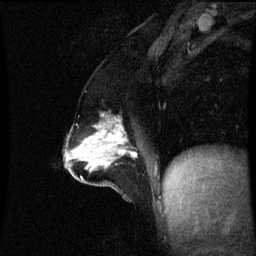
Breast MRI (dynamic contrast-enhanced), one sagittal slice. Slice 30 of 60 in the series (ordered by position). Dynamic contrast-enhanced series, image 2 of 3 at this slice position (ordered by acquisition). 1.5 T. TE 4.2 ms, TR 8.9 ms. 2.1 mm slice thickness. 256 × 256 image matrix. Patient: female, 47 years. Case-level facts recorded for this patient, not image findings: setting: breast cancer imaged before/during neoadjuvant chemotherapy; receptor status: HR-positive, HER2-negative.
Annotated regions visible in this slice (semi-automatic segmentation, software-assisted and operator-edited):
- analysis volume of interest (the breast-tissue region the enhancement analysis was run in; not a lesion): bounding box <71,120,138,163> (left, top, right, bottom; pixels)
- tumour enhancement mask (voxels above the 70 % enhancement threshold inside the analysis volume of interest): <88,124,138,157>